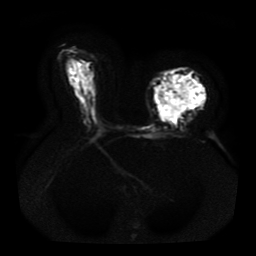
Breast MRI, one axial slice. Position 24 of 41 along the scan axis. Diffusion-weighted series; image 2 of 4 stored at this slice position (different b-values; order by instance number). 1.5 T. 256 × 256 image matrix. Female patient.
Outlined on this slice (outlined manually by an expert reader):
- tumour on diffusion-weighted imaging: bounding box (x1, y1, x2, y2) in pixels: (155, 76, 205, 121)